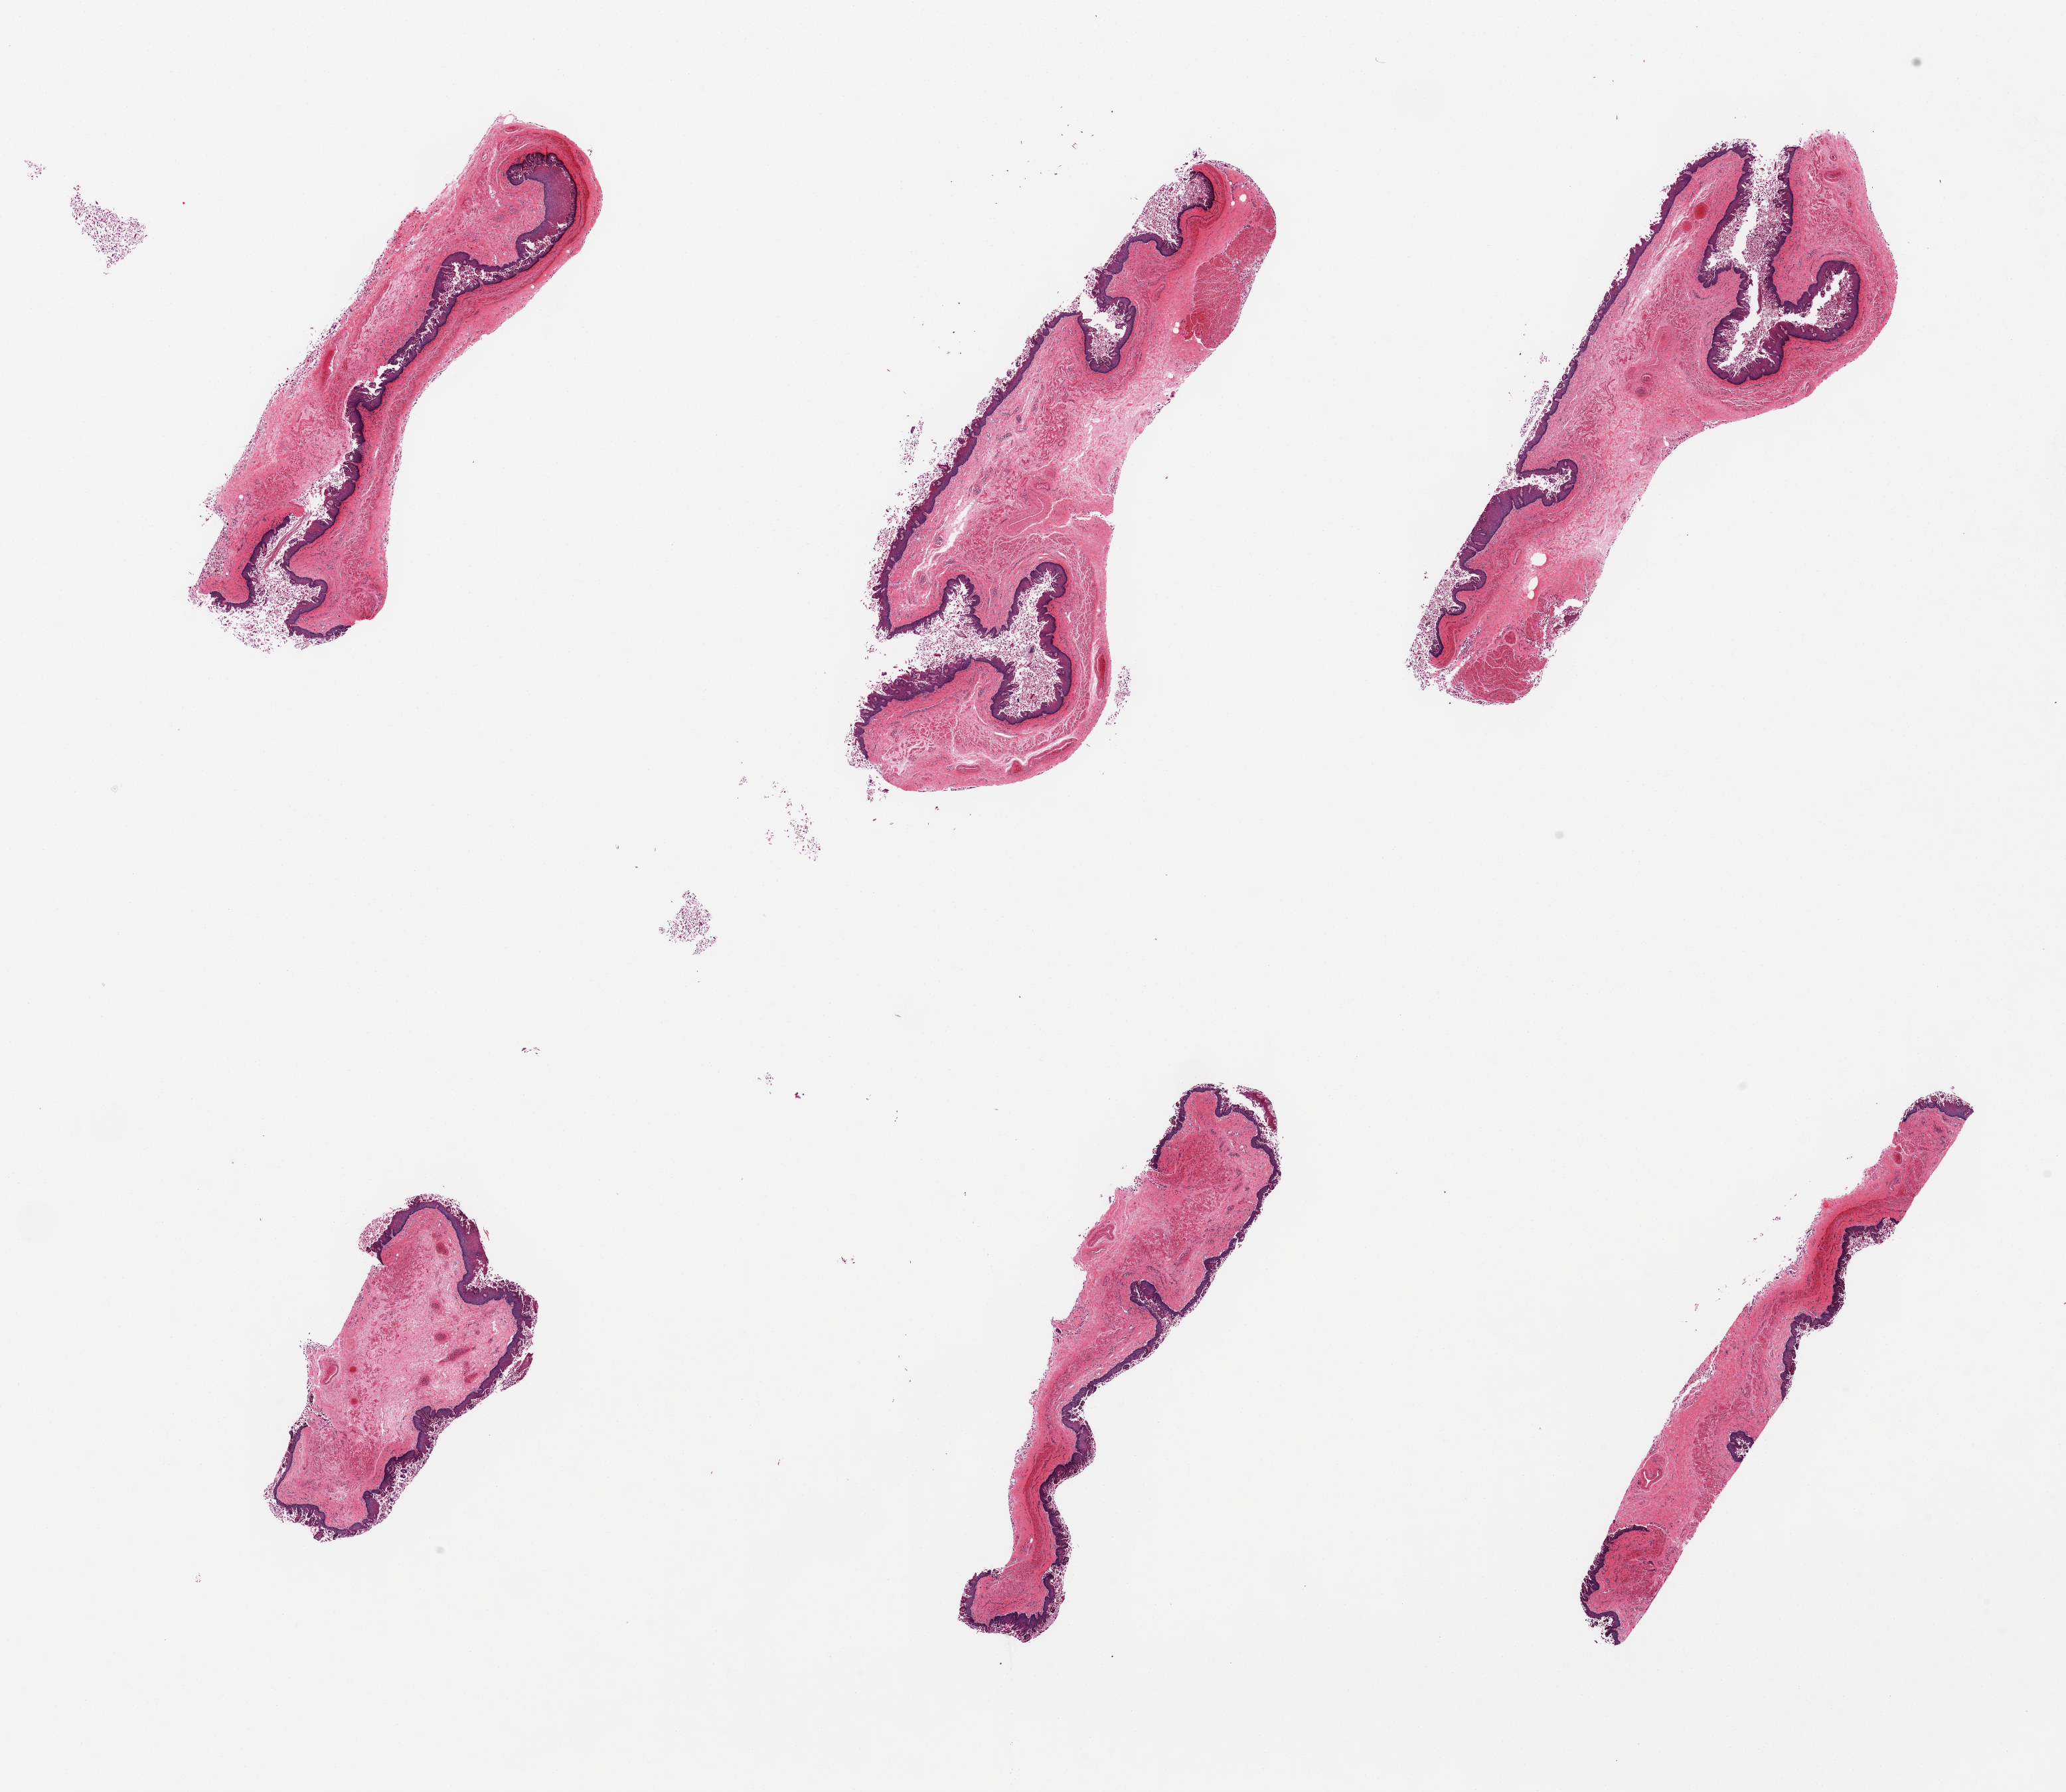
H&E whole-slide image, shown as a low-resolution overview of the whole scanned area (about 24.6 x 21.3 mm); PAXgene-fixed paraffin-embedded (PFPE) section; section of esophageal mucous membrane (target tissue); tissue donor sample. Donor sex: male.
Pathologist's review note for this sample: 6 pieces, epithelium sloughing, muscularis focally present.